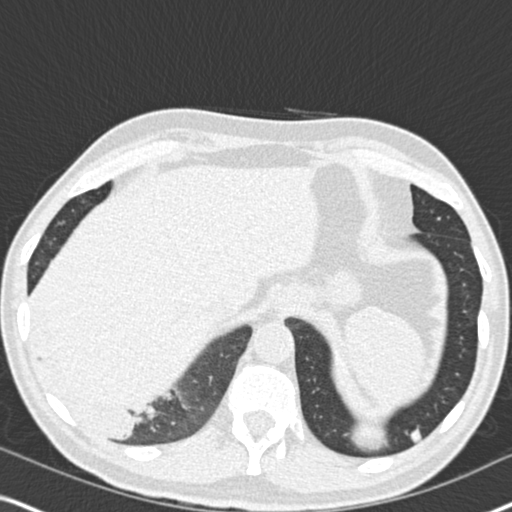
Low-dose screening chest CT, axial slice. Second annual screen. Lung window (W 1500 / L -600 HU). Standard (soft-tissue) reconstruction kernel (B30f). 512 × 512 image matrix, field of view 330 × 330 mm. Male participant, aged 61 years at enrolment. Current smoker at enrolment.
Expert reader's lesion annotation, bounding box <13,270,178,453> (left, top, right, bottom; pixels). The exam's reader record, not a measurement of the box and not confirmed to be the same lesion: non-calcified nodule or mass ≥4 mm, right lower lobe, 90 × 80 mm, soft tissue attenuation, pre-existing on the prior screen: yes; interval growth: yes. Participant outcome: lung cancer diagnosed 20 days after this screen — bronchiolo-alveolar adenocarcinoma, NOS, right lower lobe, moderately differentiated (G2), stage IIIB (AJCC 6th edition), 90 mm at pathology.